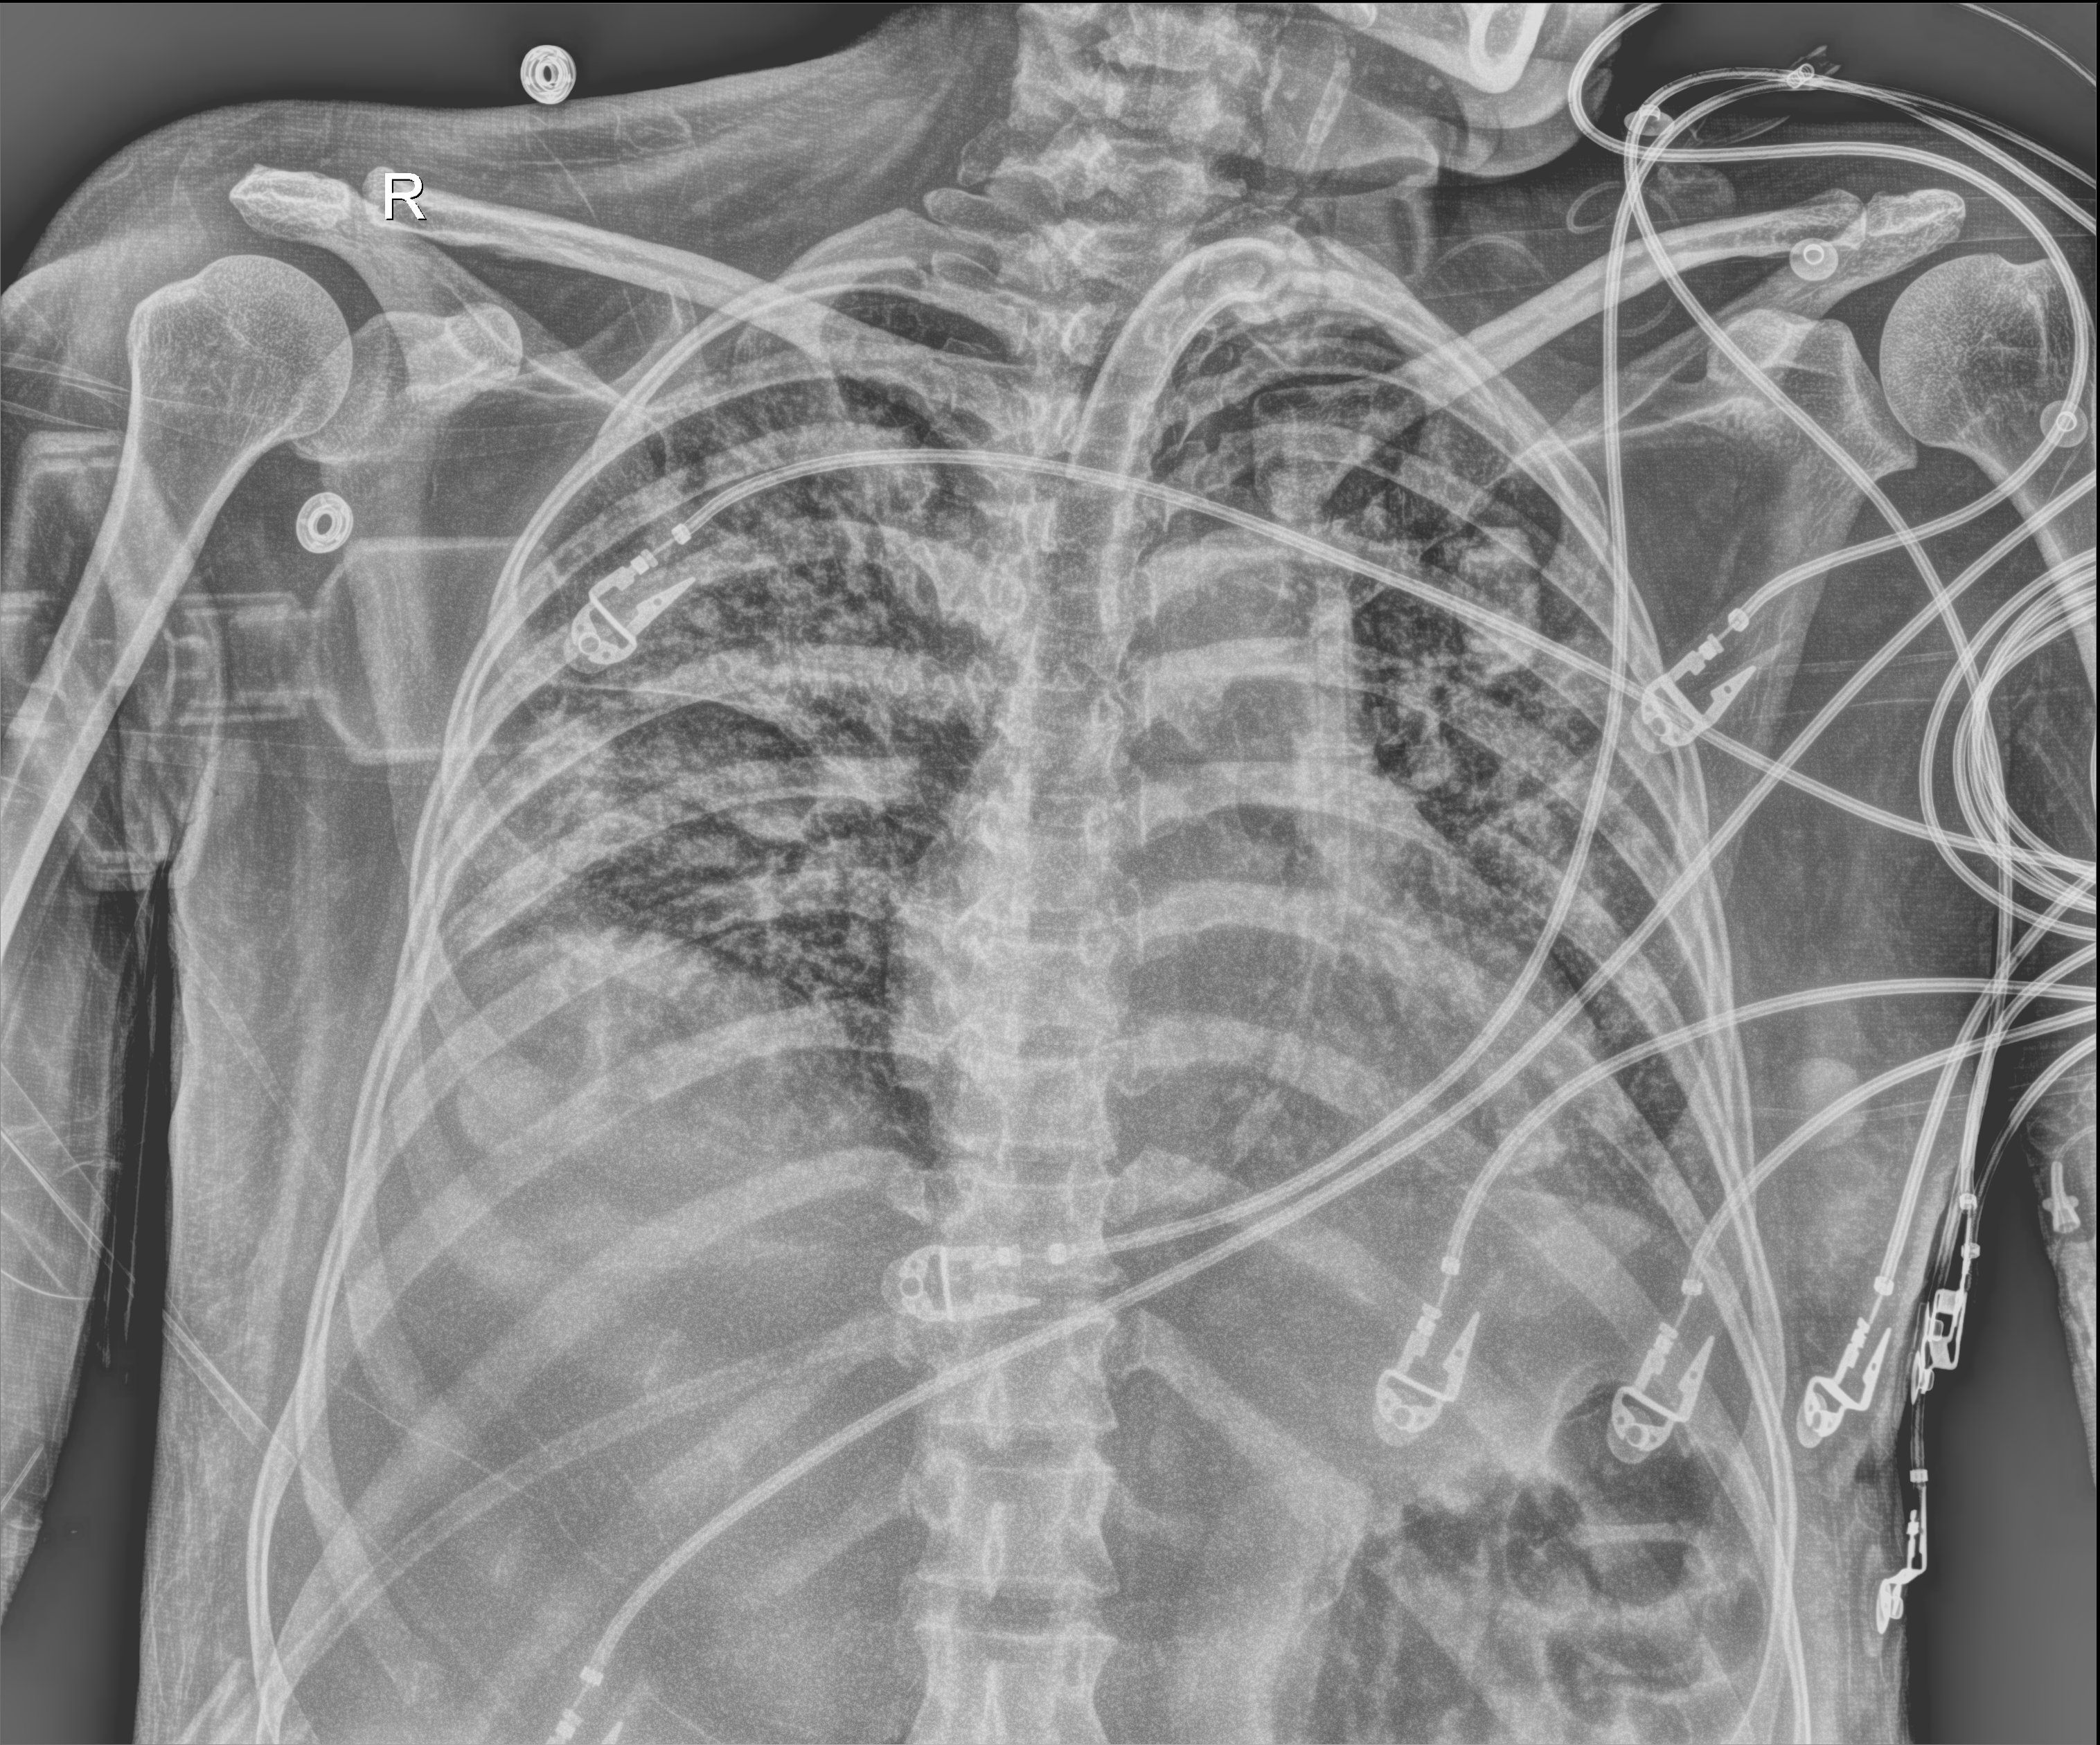
Bedside chest radiograph (digital radiography); anteroposterior (AP) projection. Female patient hospitalised with COVID-19, age 18–59 years.
Admission-level facts for this patient (not findings on this image; timing relative to this image not recorded):
- smoking status (admission record): former
- COPD (admission record): no
- admitted to intensive care during this hospital stay: yes